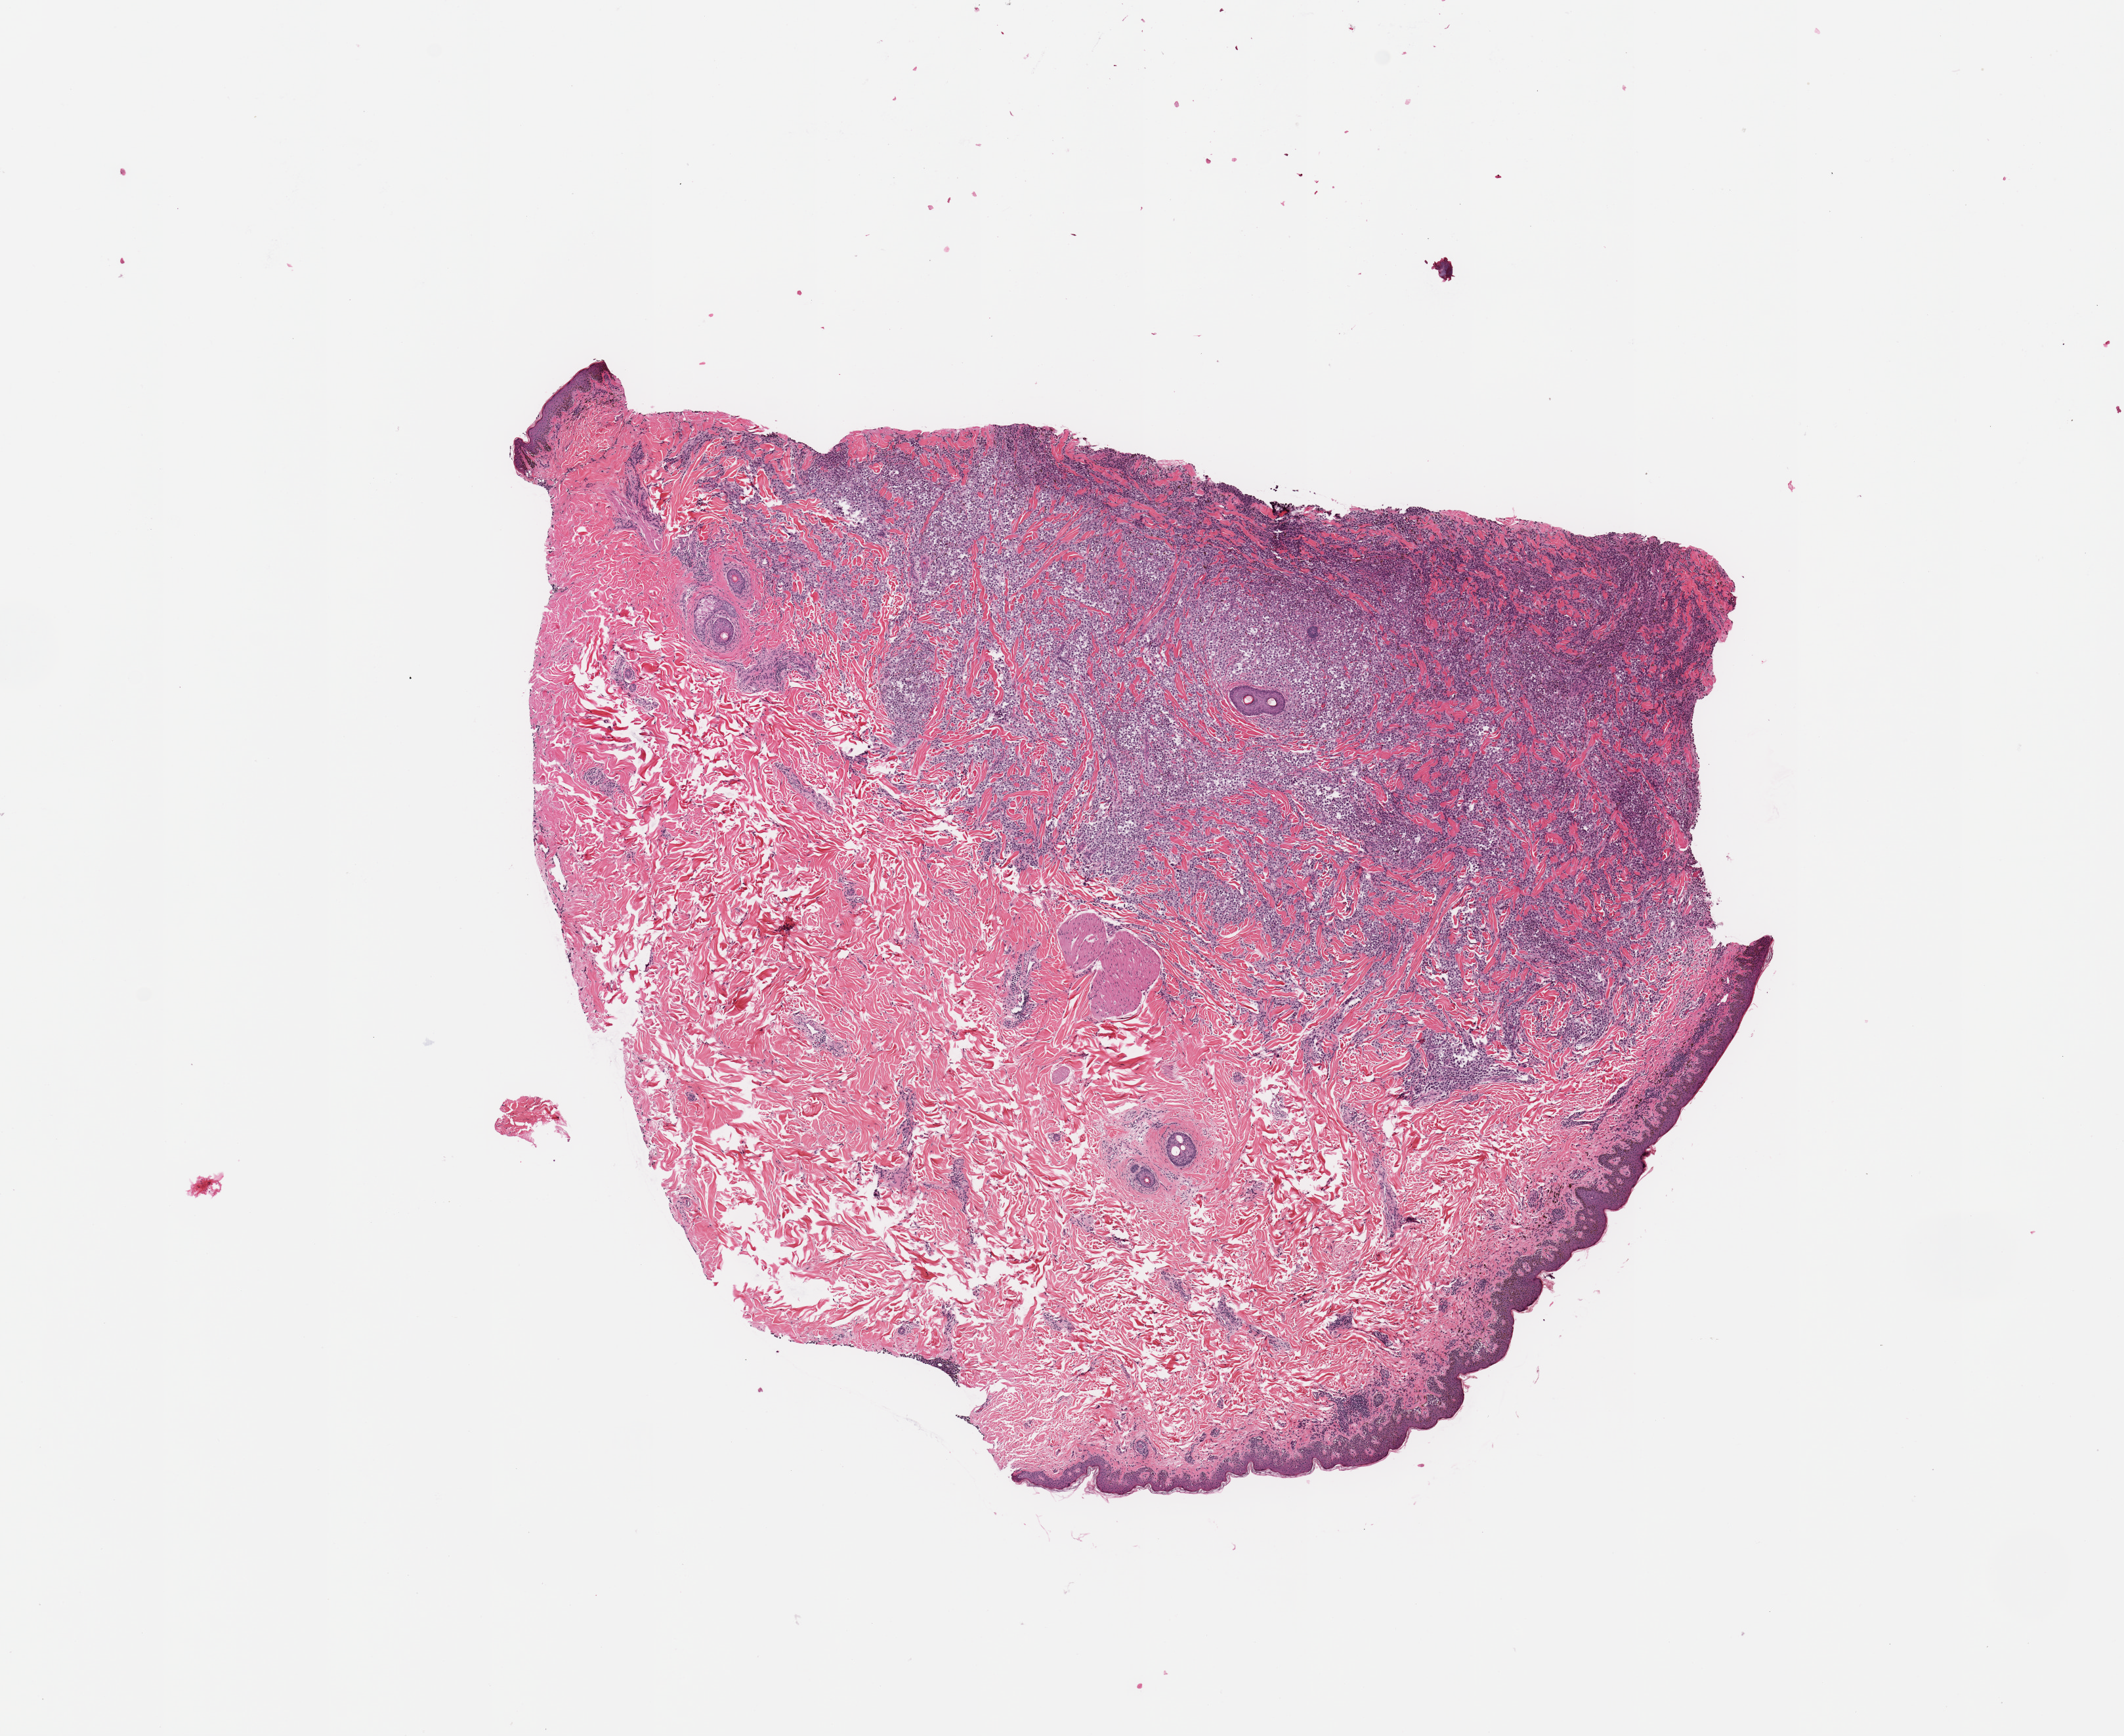
Whole-slide histology image, H&E, low-resolution overview of the scanned area, about 12.8 x 10.5 mm, melanoma tumour tissue; sampled site not recorded. Patient: female, age 69 years.
- histologic diagnosis: Malignant melanoma, NOS
- AJCC pathologic stage: IIIB
- primary tumour site (as recorded): trunk